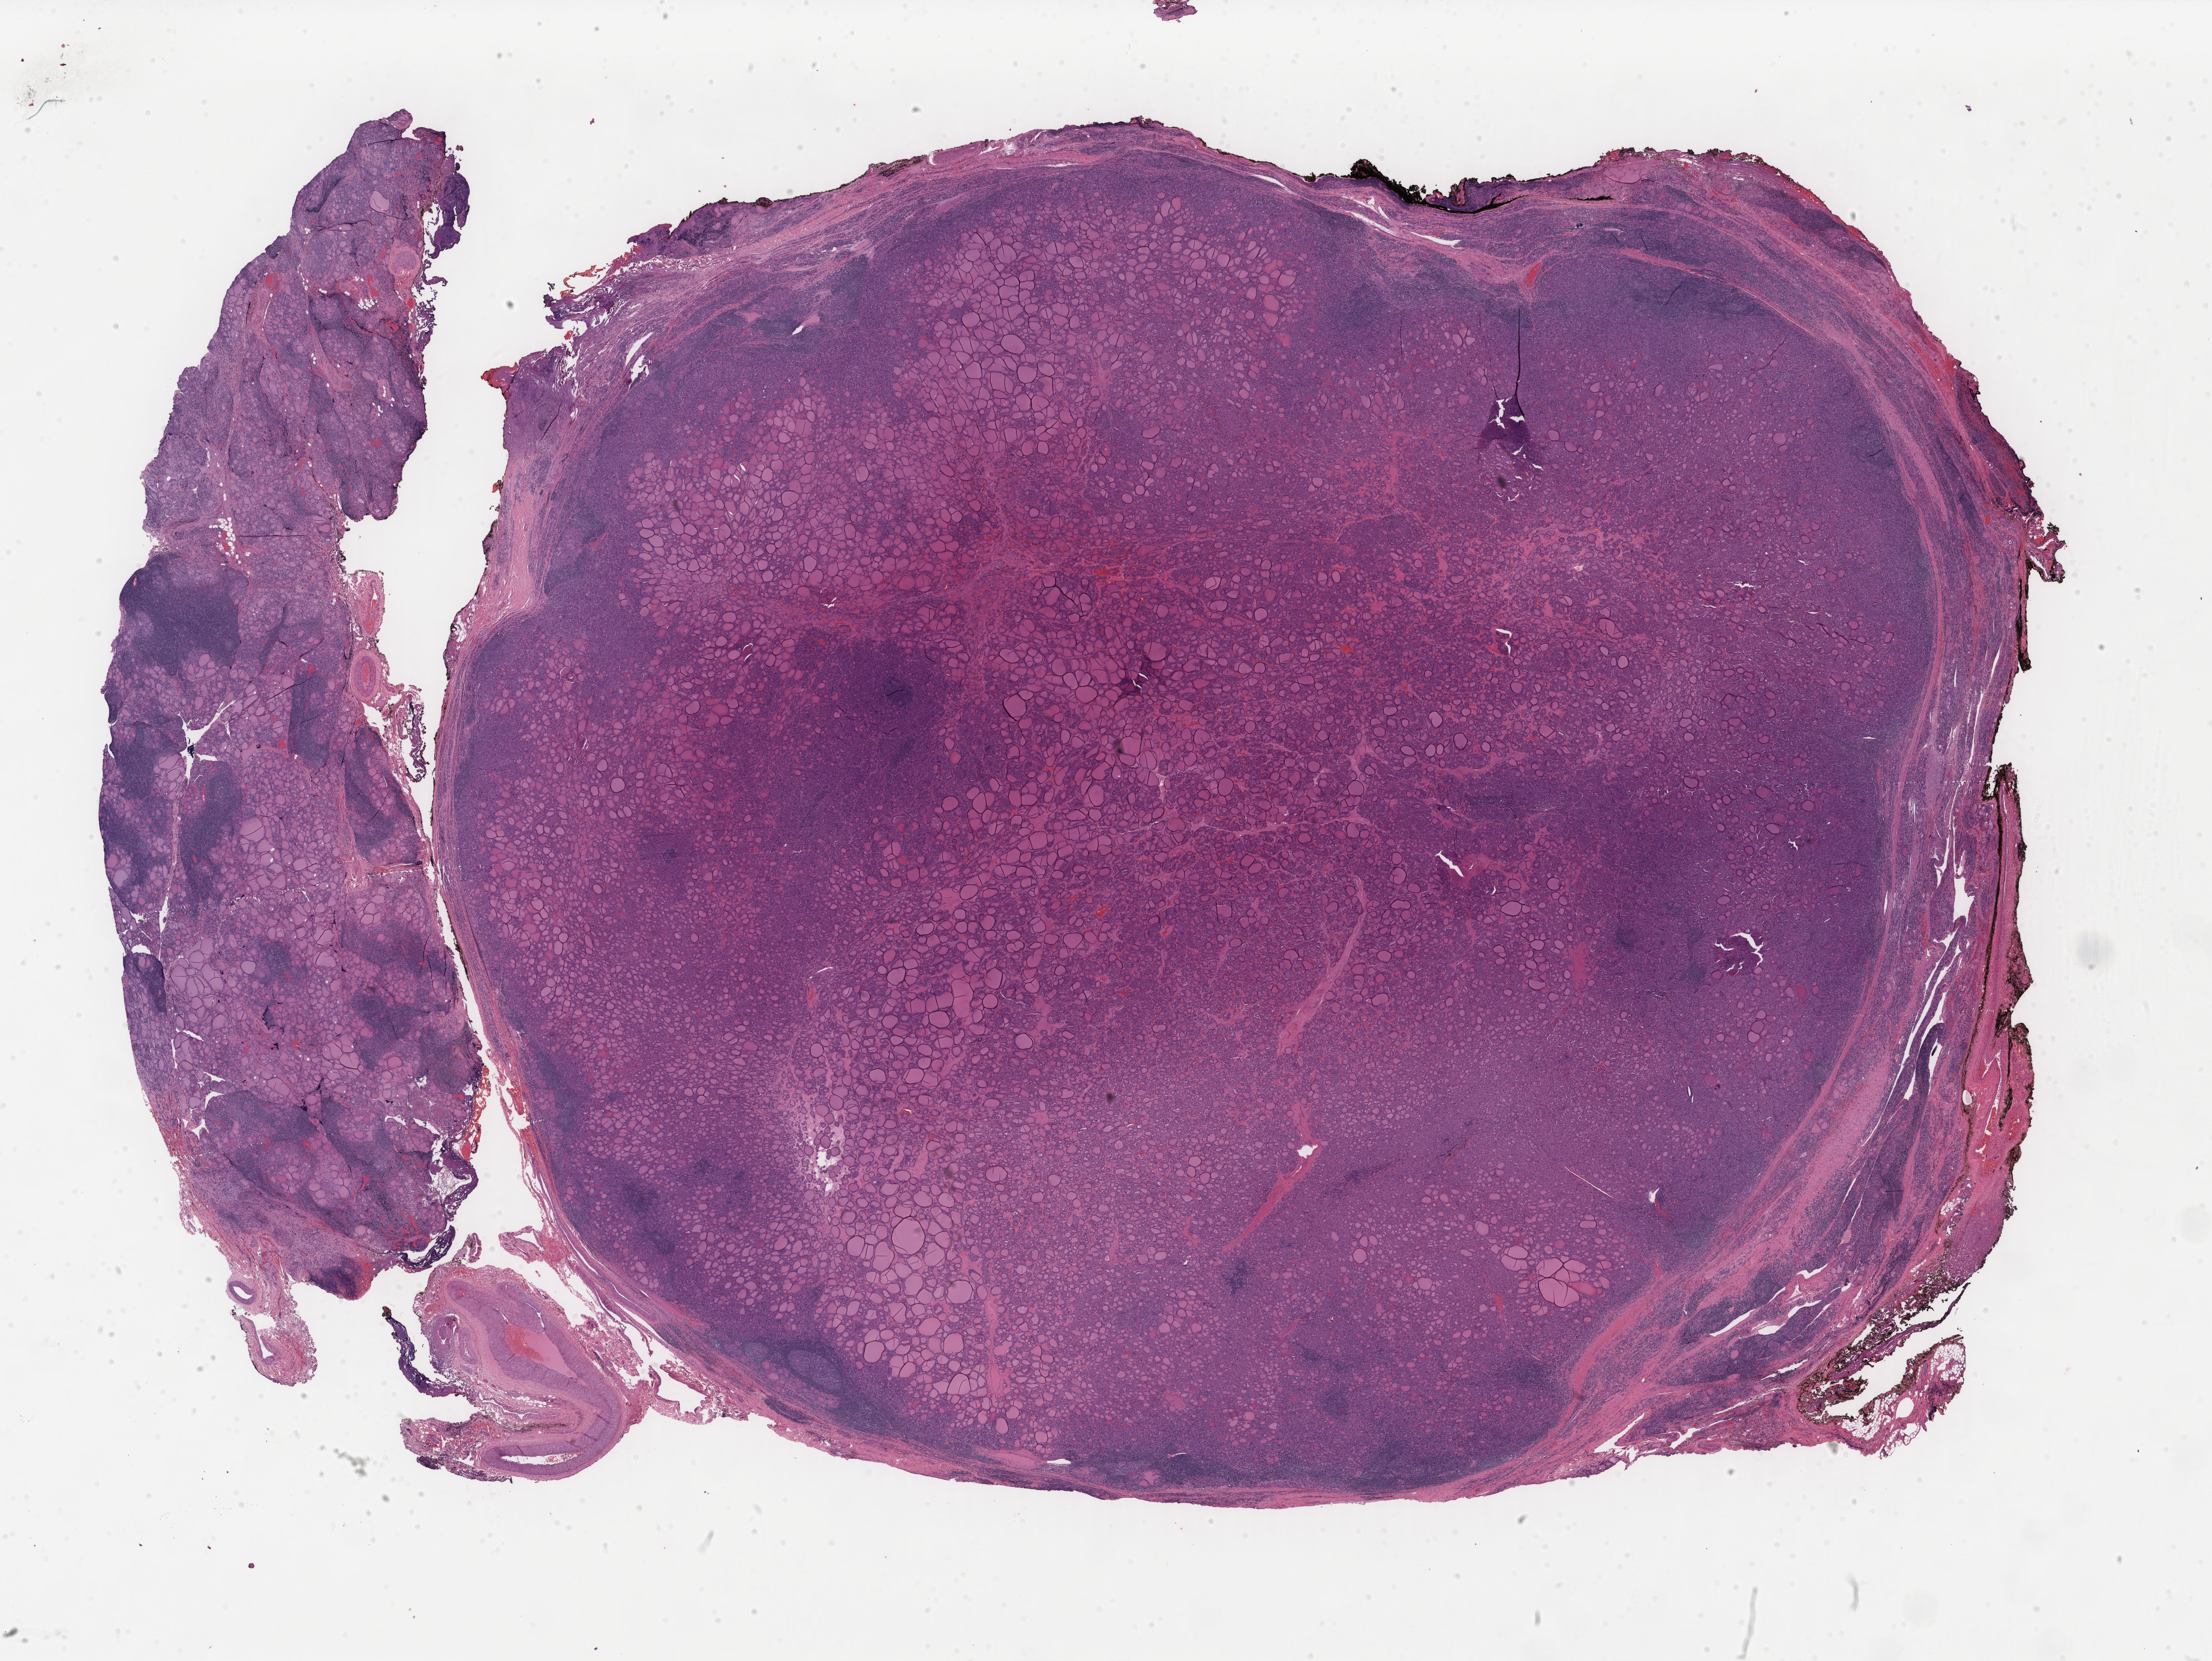
Whole-slide histology image, H&E — a low-resolution overview of the entire scanned area, about 29.3 x 22.0 mm (acquisition: 40x scan). FFPE section. Primary tumour sample from the thyroid. Female patient; age at initial diagnosis 42 years.
Laterality: right. Diagnosis: Papillary adenocarcinoma, NOS (thyroid gland). AJCC pathologic stage: I (7th edition).